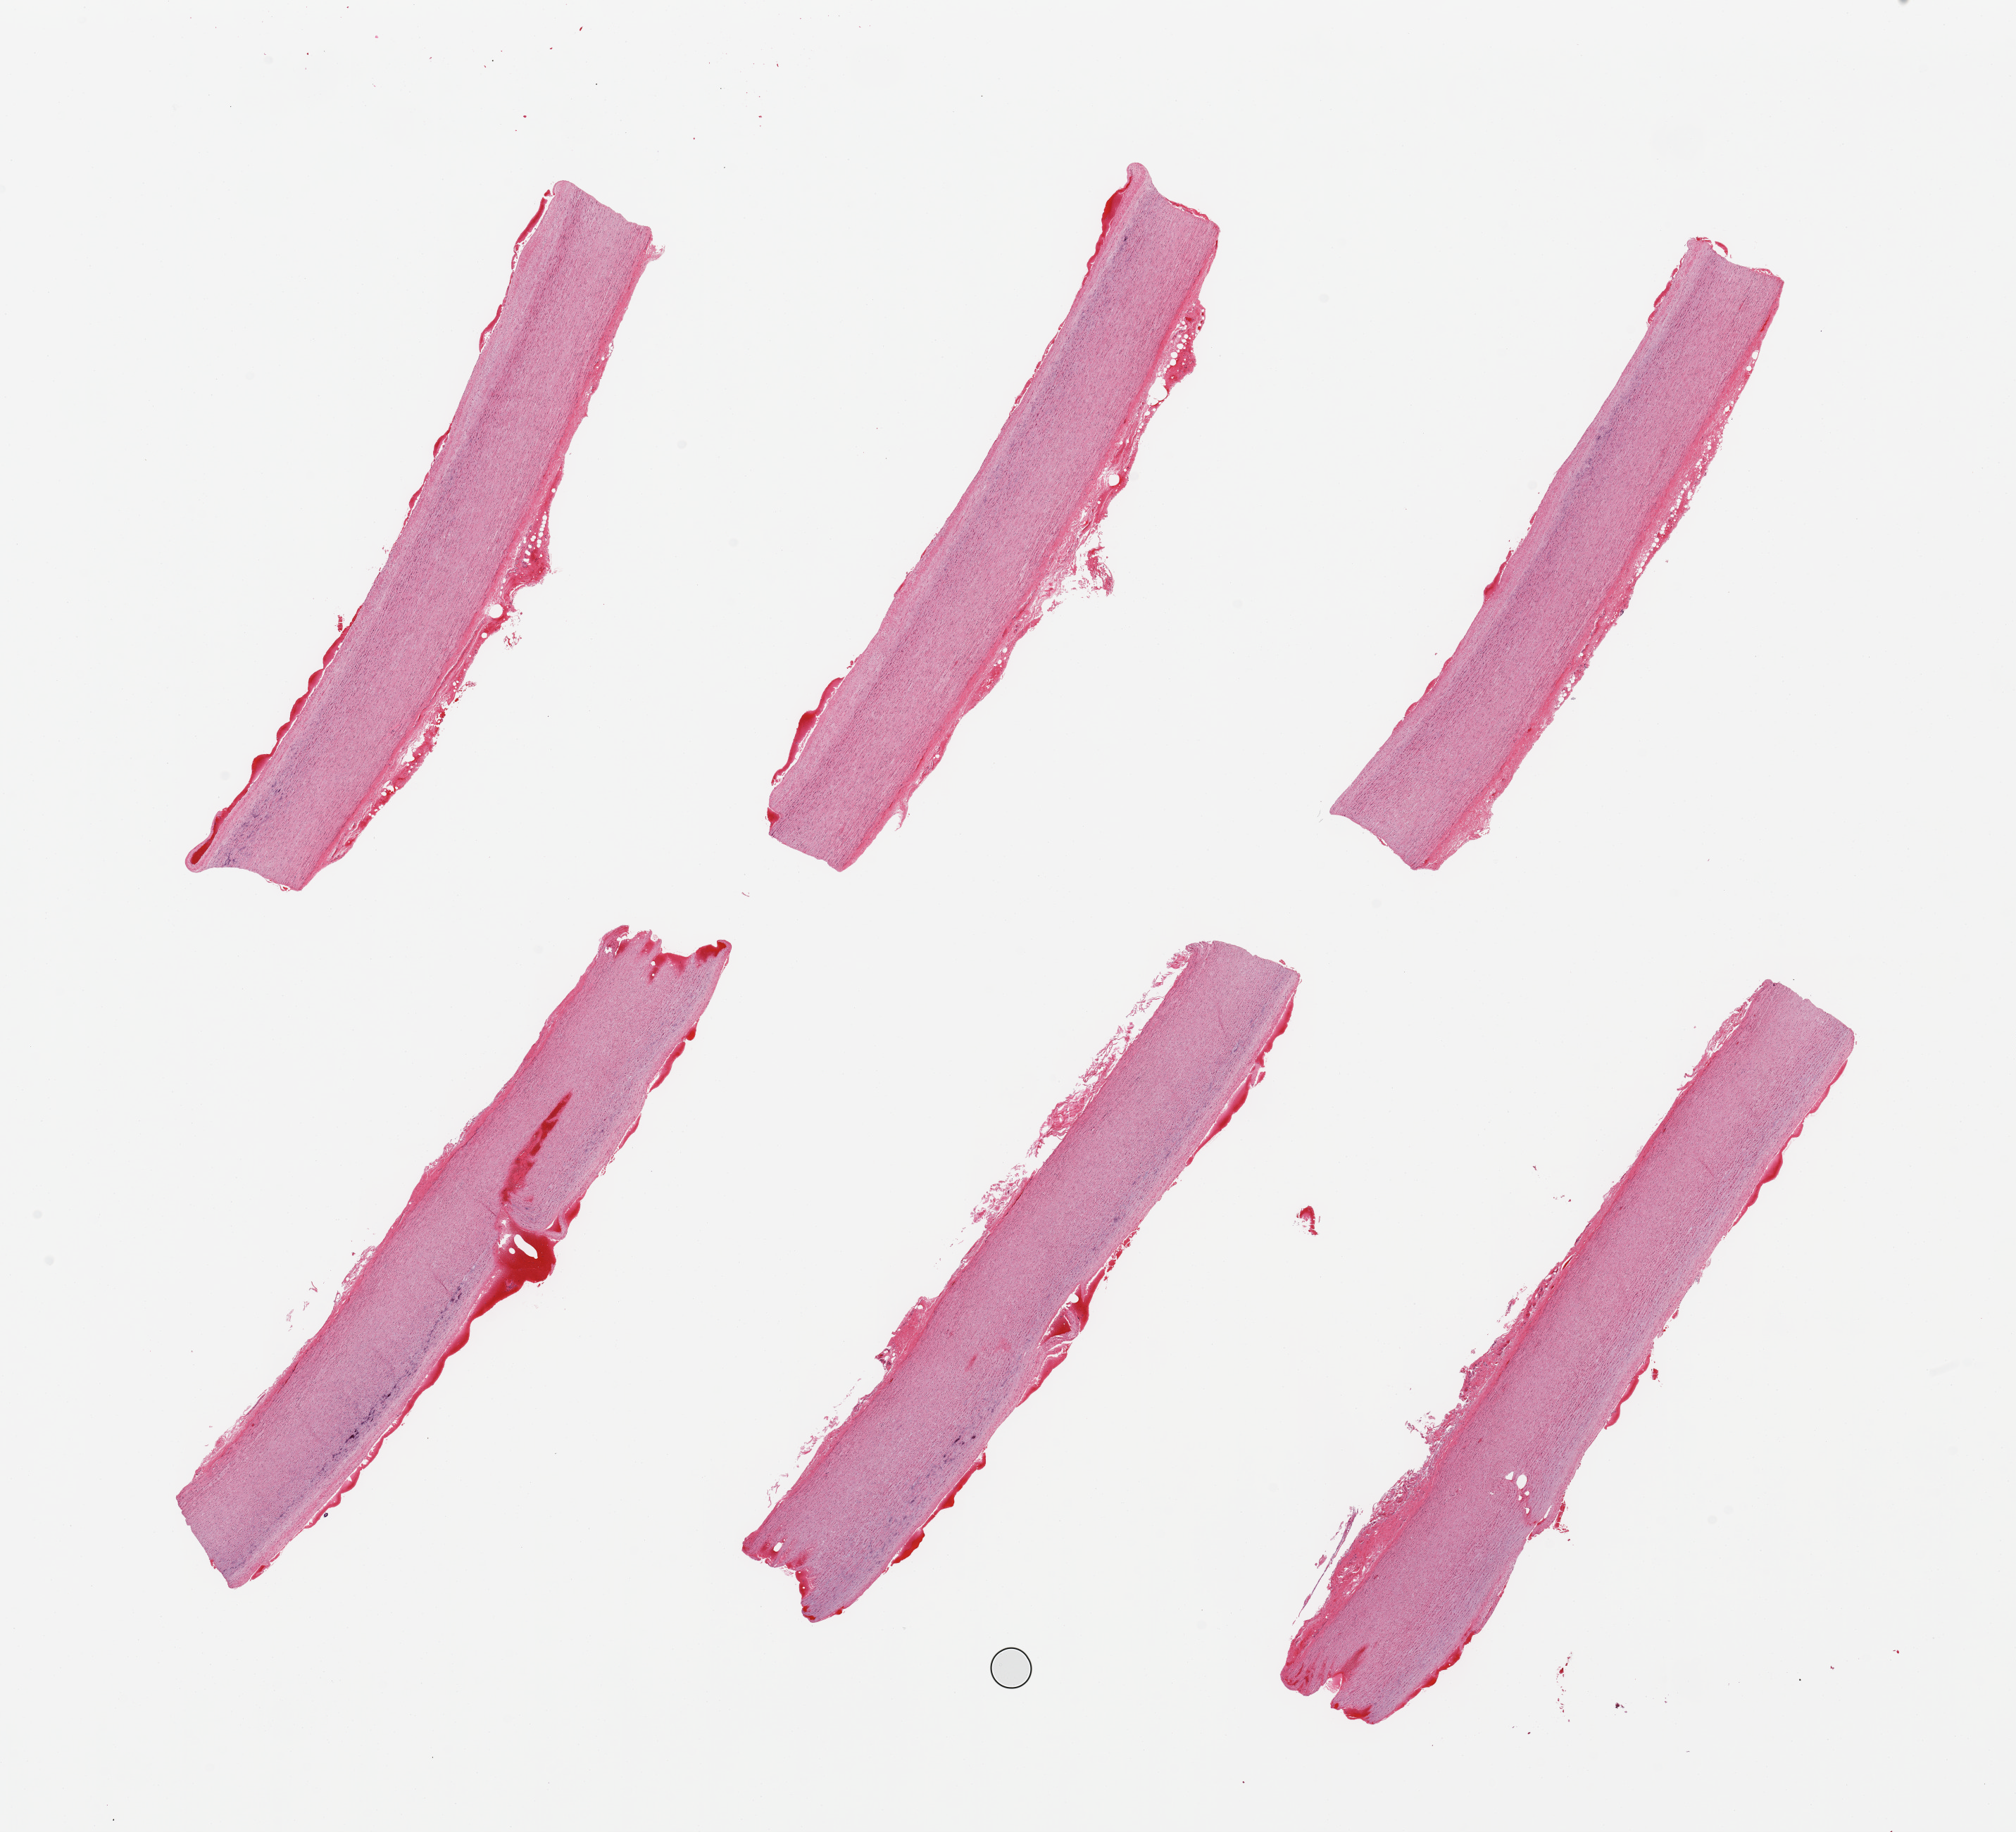
Whole-slide image, H&E stain, brightfield — low-resolution overview of the scanned area, about 22.6 x 20.6 mm (slide scanned at 20x). PAXgene-fixed paraffin-embedded (PFPE) section. Sampled site (target tissue): aorta. Tissue donor sample.
* review note (as recorded): 6 pieces, atherosis up to ~0.3mm